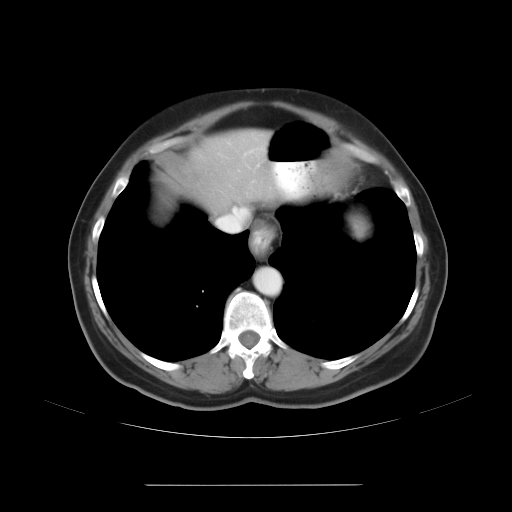
Contrast-enhanced abdominal CT, one axial slice; position 25 of 27 along the scan axis; intravenous contrast given; soft-tissue window (W 400 / L 40 HU); 7.5 mm slice thickness; 512 × 512 image matrix. Female patient, age 58 years. Case-level facts recorded for this patient, not image findings: diagnosis: colorectal cancer liver metastases, imaged before liver resection; multiple liver metastases: yes; largest metastasis: 1.9 cm; disease in both lobes: yes.
Structures marked on this image (expert manual segmentation):
- hepatic veins: box from (x=216, y=207) to (x=238, y=223) px
- liver: (x=190, y=136)–(x=275, y=208)
- planned liver remnant (the part of the liver to remain after resection): (x=190, y=135)–(x=275, y=207)